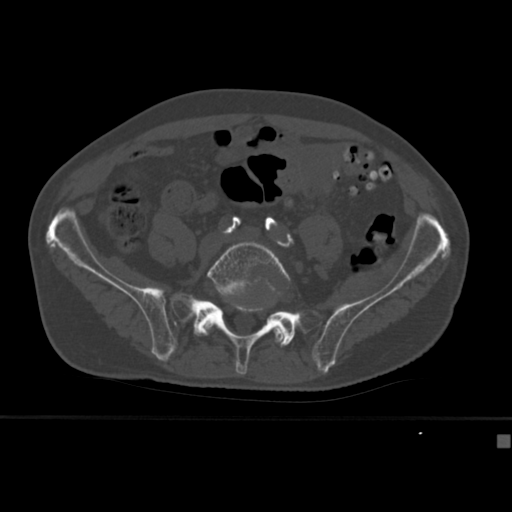
CT including the spine, one axial slice. Slice 79 of 430 in the series (ordered by position). Reconstruction kernel Br40s. 120 kVp. Bone window (W 1800 / L 400 HU). 1.5 mm slice thickness. 512 × 512 image matrix, field of view 337 × 337 mm. Patient: male, 64 years. From the clinical record (not read from this slice): primary cancer: uterus.
Annotated regions visible in this slice (semi-automatically segmented with operator editing):
- L5 vertebra: bounding box <197,241,290,347> (left, top, right, bottom; pixels)